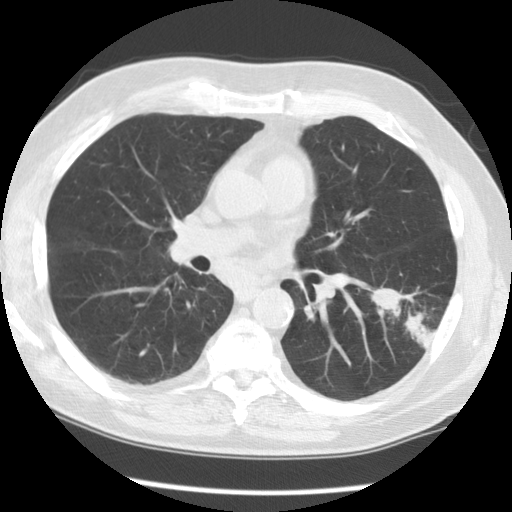
Chest CT (low-dose screening protocol), one axial image, baseline annual screen, lung window (W 1500 / L -600 HU), slice 57 of 130 in the series, 512 × 512 image matrix. Male participant, aged 71 years at enrolment. Former smoker at enrolment.
Expert reader's lesion annotation, bounding box <370,276,460,365> (left, top, right, bottom; pixels). The screening reader recorded 3 non-calcified nodules or masses ≥4 mm on this exam (left lower lobe, right upper lobe, right upper lobe); which of them this box marks is not recorded.